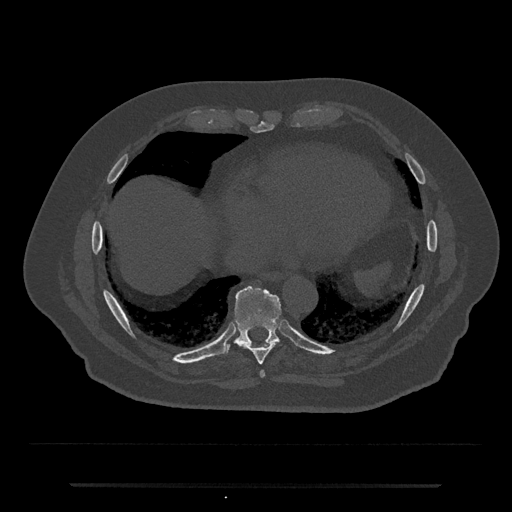
CT including the spine, one axial slice. Position 781 of 797 along the scan axis. 120 kVp. Bone window (W 1800 / L 400 HU). 512 × 512 image matrix. Male patient, age 80 years. From the clinical record (not read from this slice): primary cancer: prostate.
Structures marked on this image (semi-automatically segmented with operator editing):
- T8 vertebra: bounding box (x1, y1, x2, y2) in pixels: (241, 342, 278, 365)
- T9 vertebra: (218, 287, 281, 355)